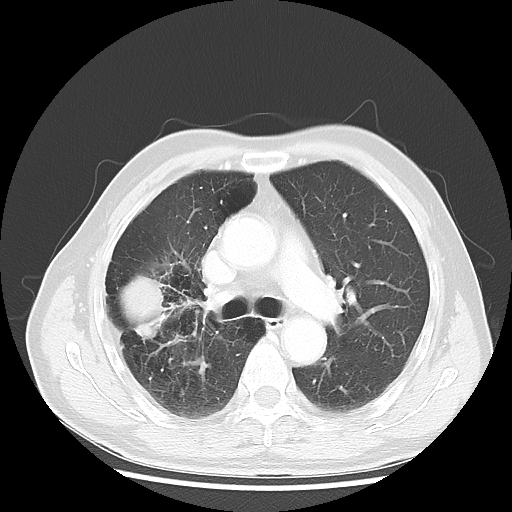
Chest CT, one axial slice. Position 31 of 50 along the scan axis. Reconstruction kernel LUNG. Lung window (W 1500 / L -600 HU). 512 × 512 image matrix. Patient: male, 69 years. Case-level facts recorded for this patient, not image findings: clinical TNM (as recorded): T3 N0 M0; histopathological grade: G3.
Annotated regions visible in this slice (bounding box drawn by a radiologist):
- lung tumour (recorded histology: adenocarcinoma): bounding box <115,273,178,353> (left, top, right, bottom; pixels)